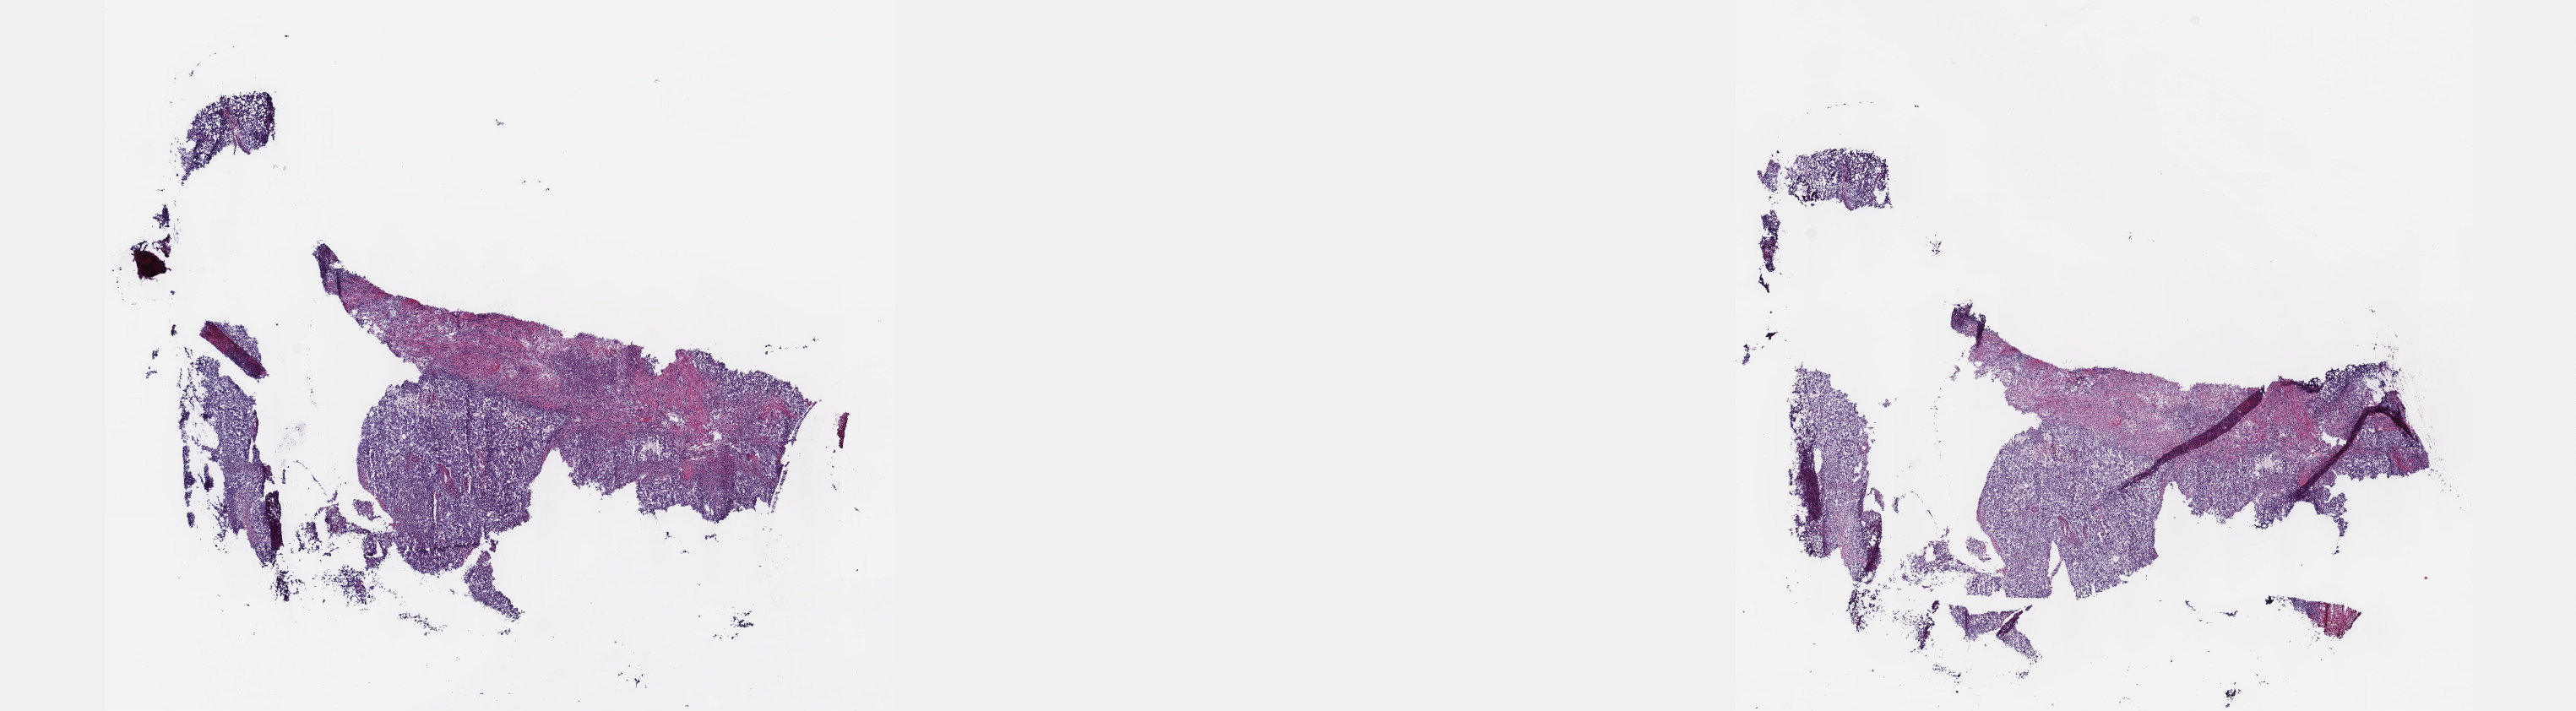
Hematoxylin and eosin (H&E) stained whole-slide image, low-resolution overview of the scanned area, about 24.6 x 6.8 mm. Frozen section. Sample: primary tumour, testis. Male patient; age at initial diagnosis 28 years. Composition of this section per pathologist review: tumour cells 80%, tumour nuclei 80%.
Histologic diagnosis: Mixed germ cell tumor.